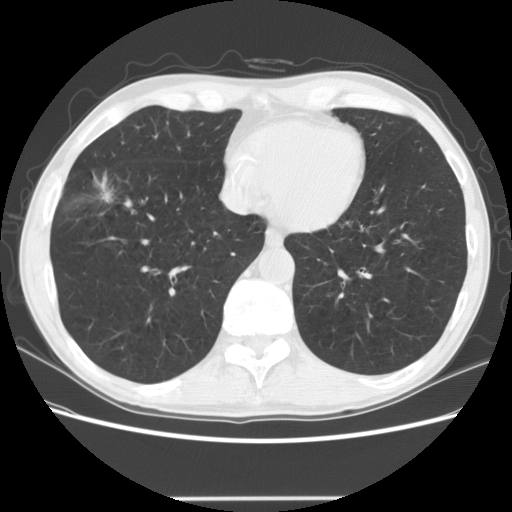
Chest CT (low-dose screening protocol), one axial image, baseline screening round, lung window (W 1500 / L -600 HU), 2.5 mm slice thickness, slice 97 of 145 in the series. Male participant, aged 69 years at enrolment. Current smoker at enrolment.
Expert-annotated lung lesion, bounding box (x1, y1, x2, y2) in pixels: (75, 161, 127, 210). The exam's reader record, not a measurement of the box and not confirmed to be the same lesion: non-calcified nodule or mass ≥4 mm, right middle lobe, 20 × 14 mm, spiculated (stellate) margins, mixed attenuation. Later outcome: lung cancer diagnosed 86 days after this screen — squamous cell carcinoma, NOS, right middle lobe, poorly differentiated (G3), stage IA (AJCC 6th edition), 15 mm at pathology.